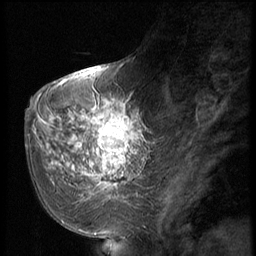
Breast MRI (dynamic contrast-enhanced), one sagittal slice. Position 21 of 56 along the scan axis. Dynamic contrast-enhanced series, image 2 of 2 at this slice position (ordered by acquisition). 1.5 T. TE 4.2 ms, TR 9 ms. 256 × 256 image matrix, field of view 180 × 180 mm. Patient: female, 51 years. Case-level facts recorded for this patient, not image findings: setting: breast cancer imaged before/during neoadjuvant chemotherapy; receptor status: triple-negative.
Structures marked on this image (semi-automatically segmented with operator editing):
- analysis volume of interest (the breast-tissue region the enhancement analysis was run in; not a lesion): box from (x=60, y=98) to (x=147, y=197) px
- tumour enhancement mask (voxels above the 140 % enhancement threshold inside the analysis volume of interest): (x=66, y=102)–(x=145, y=195)